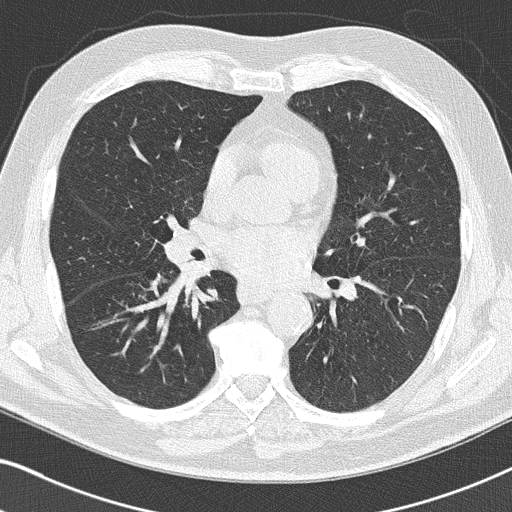
Chest CT (low-dose screening protocol), one axial image. Third annual screen. Lung window (W 1500 / L -600 HU). 2 mm slice thickness. Lung (sharp) reconstruction kernel (B50f). Male participant, aged 66 years at enrolment.
- Expert reader's lesion annotation, bounding box [x1, y1, x2, y2] px = [137, 267, 229, 330].
- Reader record for this screening exam (exam-level; its link to the box is not recorded): non-calcified nodule or mass ≥4 mm, right upper lobe, 5 × 4 mm, smooth margins, pre-existing on the prior screen: yes; interval growth: no.
- Official screen result: positive, other.
- Lung cancer was diagnosed 38 days after this screen: squamous cell carcinoma, NOS, right lower lobe, poorly differentiated (G3), stage IIA (AJCC 6th edition), 22 mm at pathology.